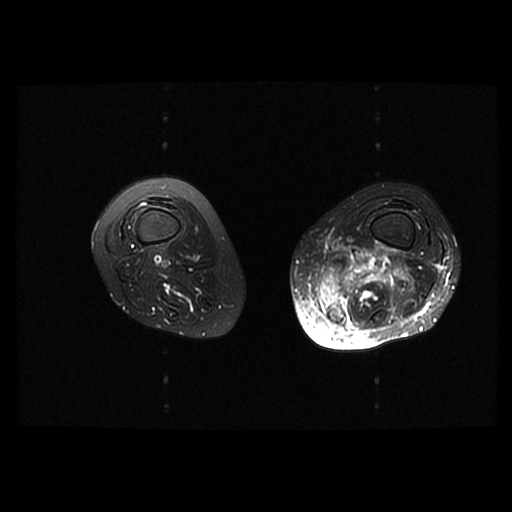
MRI of an extremity soft-tissue mass, one axial slice; slice 19 of 42 in the series (ordered by position); T2-weighted fat-saturated; 6 mm slice thickness; 512 × 512 image matrix, field of view 420 × 420 mm. Female patient. From the clinical record (not read from this slice): histological type: pleomorphic leiomyosarcoma; grade: high; site of the primary tumour: left thigh.
Annotated regions visible in this slice (manually delineated by an expert):
- gross tumour volume including surrounding oedema: bounding box (x1, y1, x2, y2) in pixels: (319, 247, 407, 325)